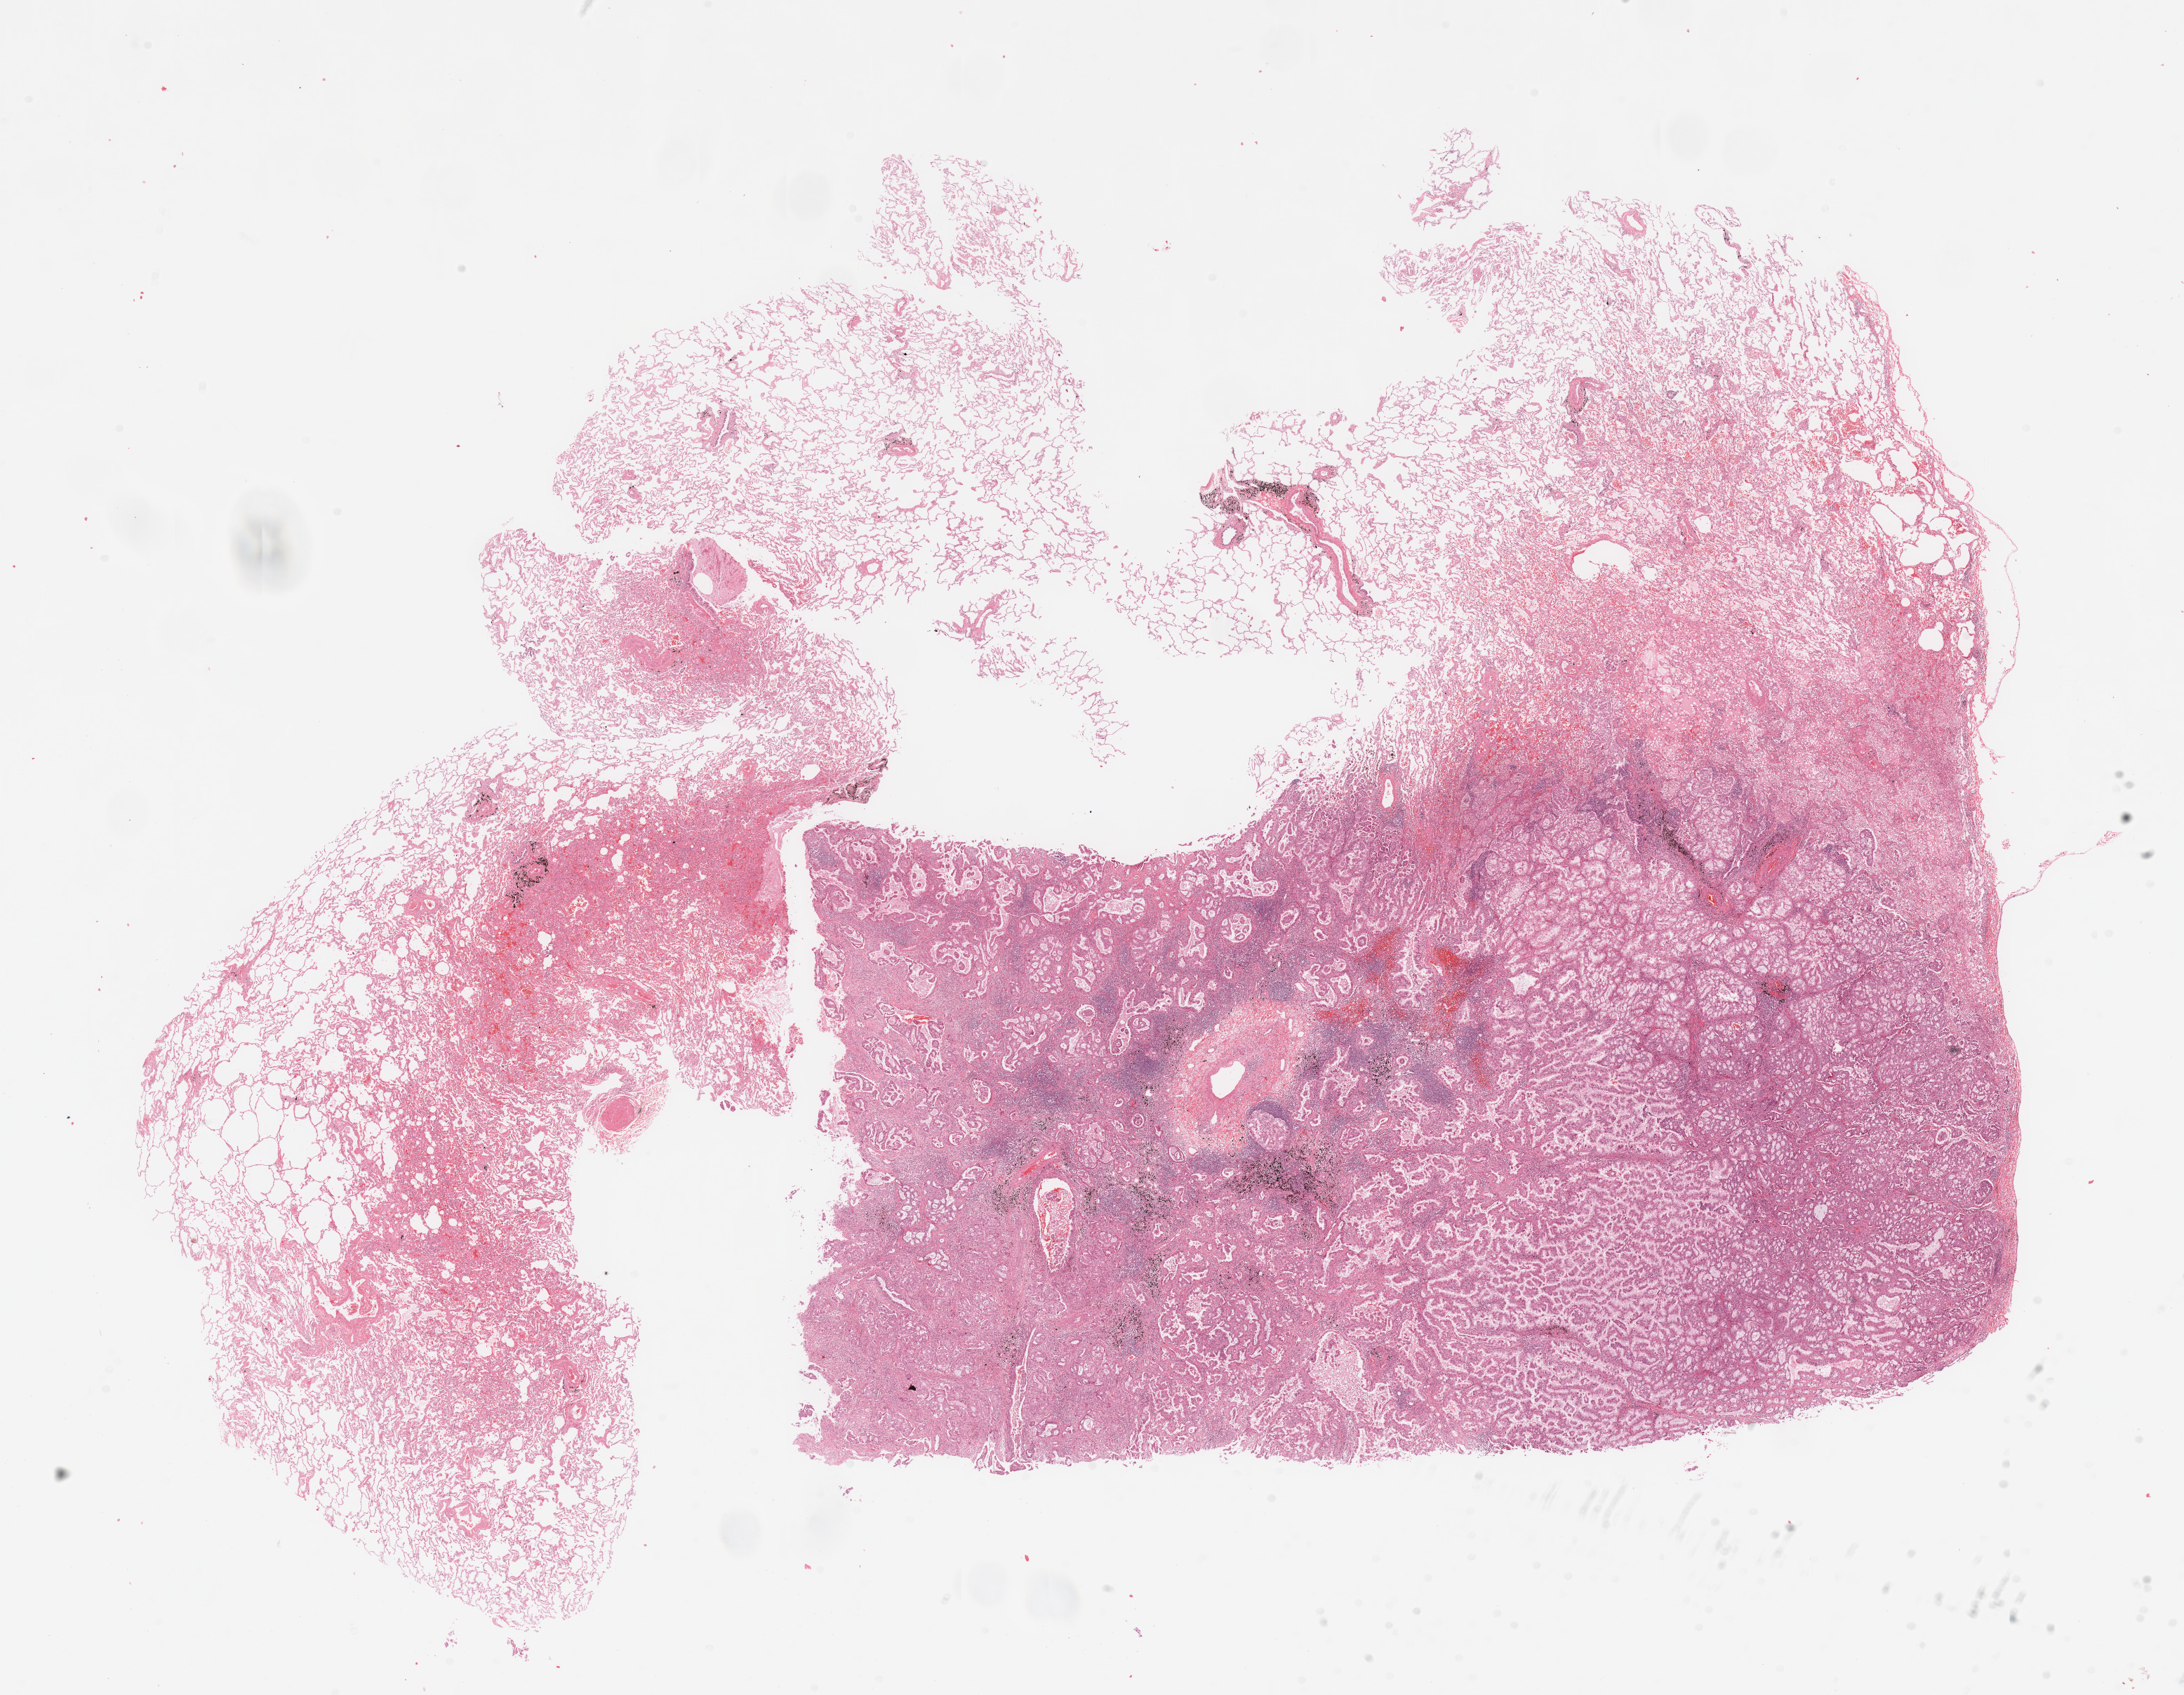
H&E whole-slide image, shown as a low-resolution overview of the whole scanned area (about 24.6 x 19.1 mm, acquisition: 20x scan); lung, tumour tissue. Patient: female, age 48 years. Histologic grade: G2 (moderately differentiated).
Primary tumour site (as recorded): right lower lobe. Histologic diagnosis: Adenocarcinoma, NOS. AJCC pathologic stage: IA.